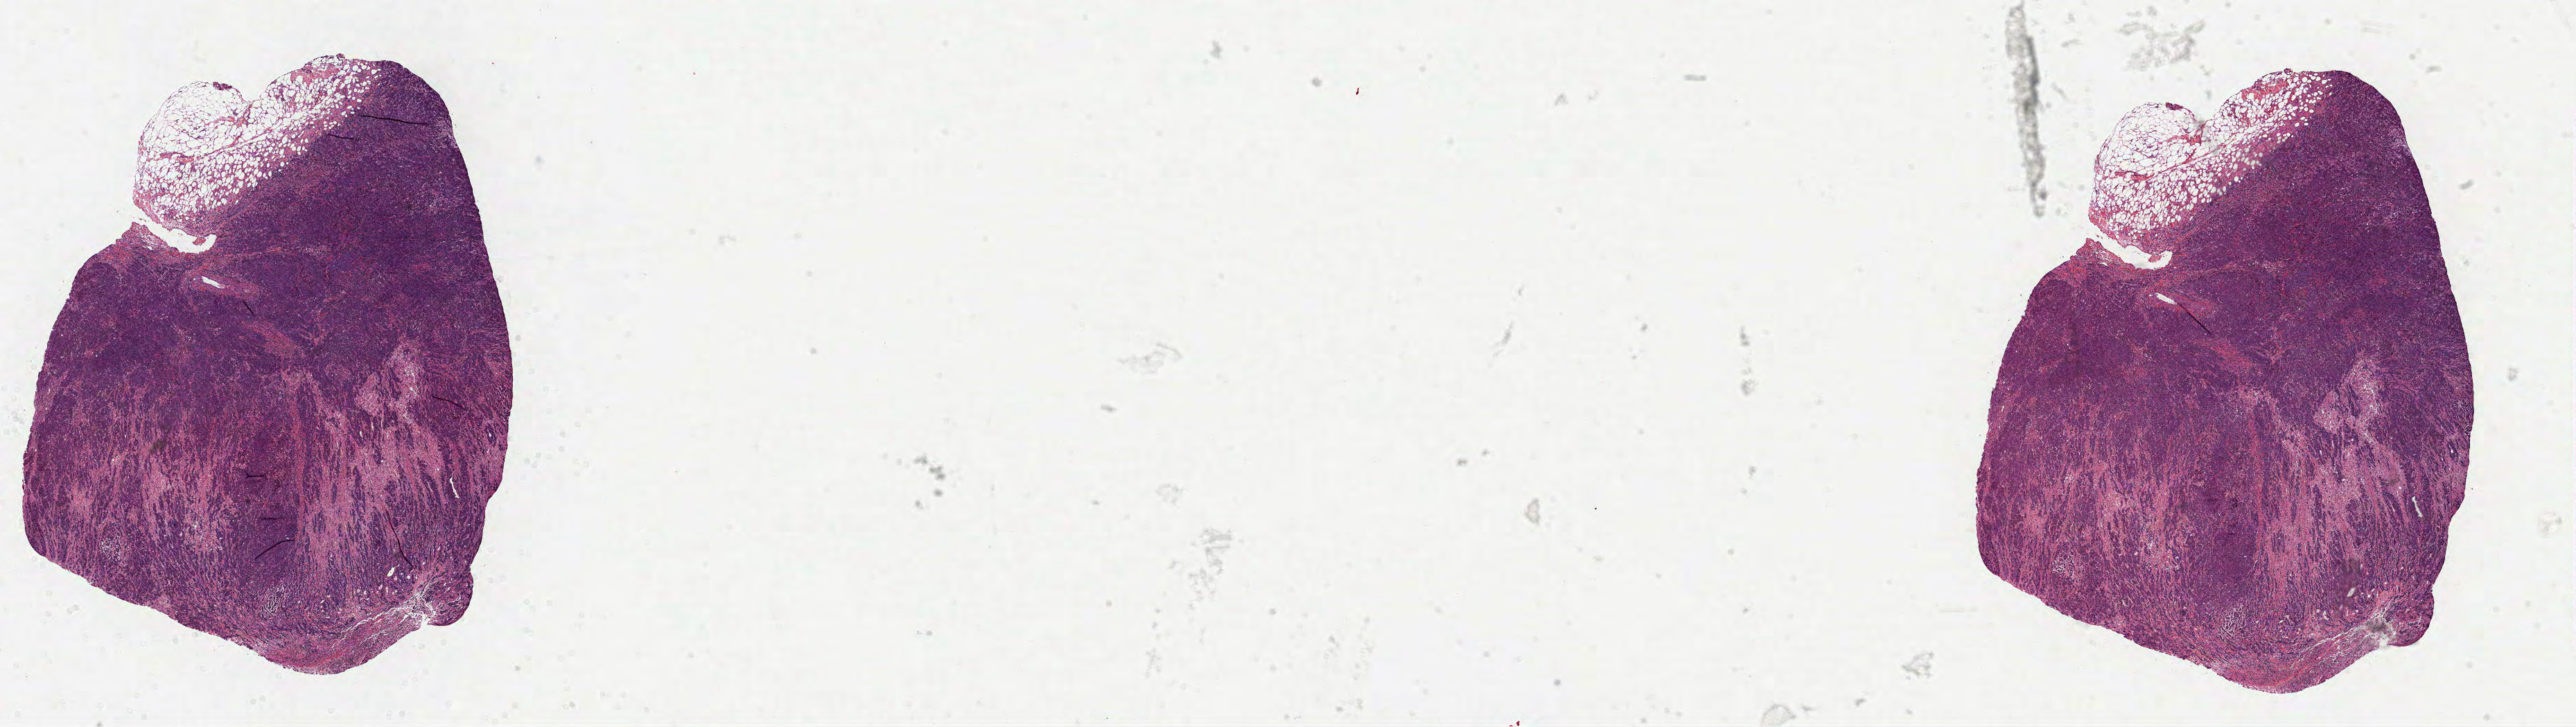
Hematoxylin and eosin (H&E) stained whole-slide image — shown as a low-resolution overview of the whole scanned area (about 30.0 x 8.5 mm, from a 40x scan). Formalin-fixed paraffin-embedded (FFPE) diagnostic section. Colon, primary tumour sample. Female patient; age at initial diagnosis 75 years.
TNM: T4 N0 M0. AJCC pathologic stage: IIB. Lymph nodes positive (case pathology): 0 of 15 examined. Histologic diagnosis: Adenocarcinoma, NOS.